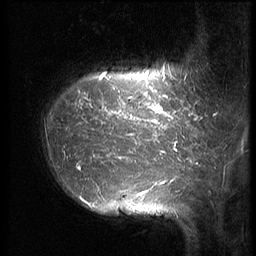
Breast MRI (dynamic contrast-enhanced), one sagittal slice. Position 13 of 64 along the scan axis. 3 images stored at this slice position (order not interpretable as contrast timing). 1.5 T. TE 4.2 ms, TR 9 ms. 2.5 mm slice thickness. 256 × 256 image matrix, field of view 180 × 180 mm. Female patient, age 39 years. Case-level facts recorded for this patient, not image findings: setting: breast cancer imaged before/during neoadjuvant chemotherapy; receptor status: HER2-positive.
Annotated regions visible in this slice (semi-automatically segmented with operator editing):
- analysis volume of interest (the breast-tissue region the enhancement analysis was run in; not a lesion): bounding box <39,47,210,239> (left, top, right, bottom; pixels)
- tumour enhancement mask (voxels above the 140 % enhancement threshold inside the analysis volume of interest): <75,72,205,203>